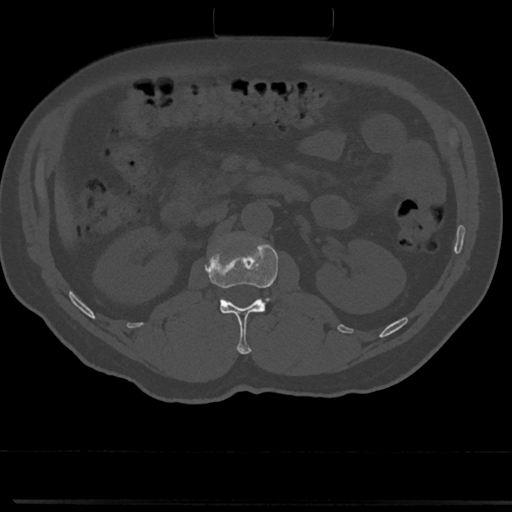
CT including the spine, one axial slice. Slice 67 of 817 in the series (ordered by position). Reconstruction kernel Br40s/3. Bone window (W 1800 / L 400 HU). 0.5 mm slice thickness. 512 × 512 image matrix. Patient: male, 61 years. From the clinical record (not read from this slice): primary cancer: prostate.
Annotated regions visible in this slice (semi-automatic segmentation, software-assisted and operator-edited):
- L1 vertebra: box from (x=206, y=235) to (x=301, y=354) px